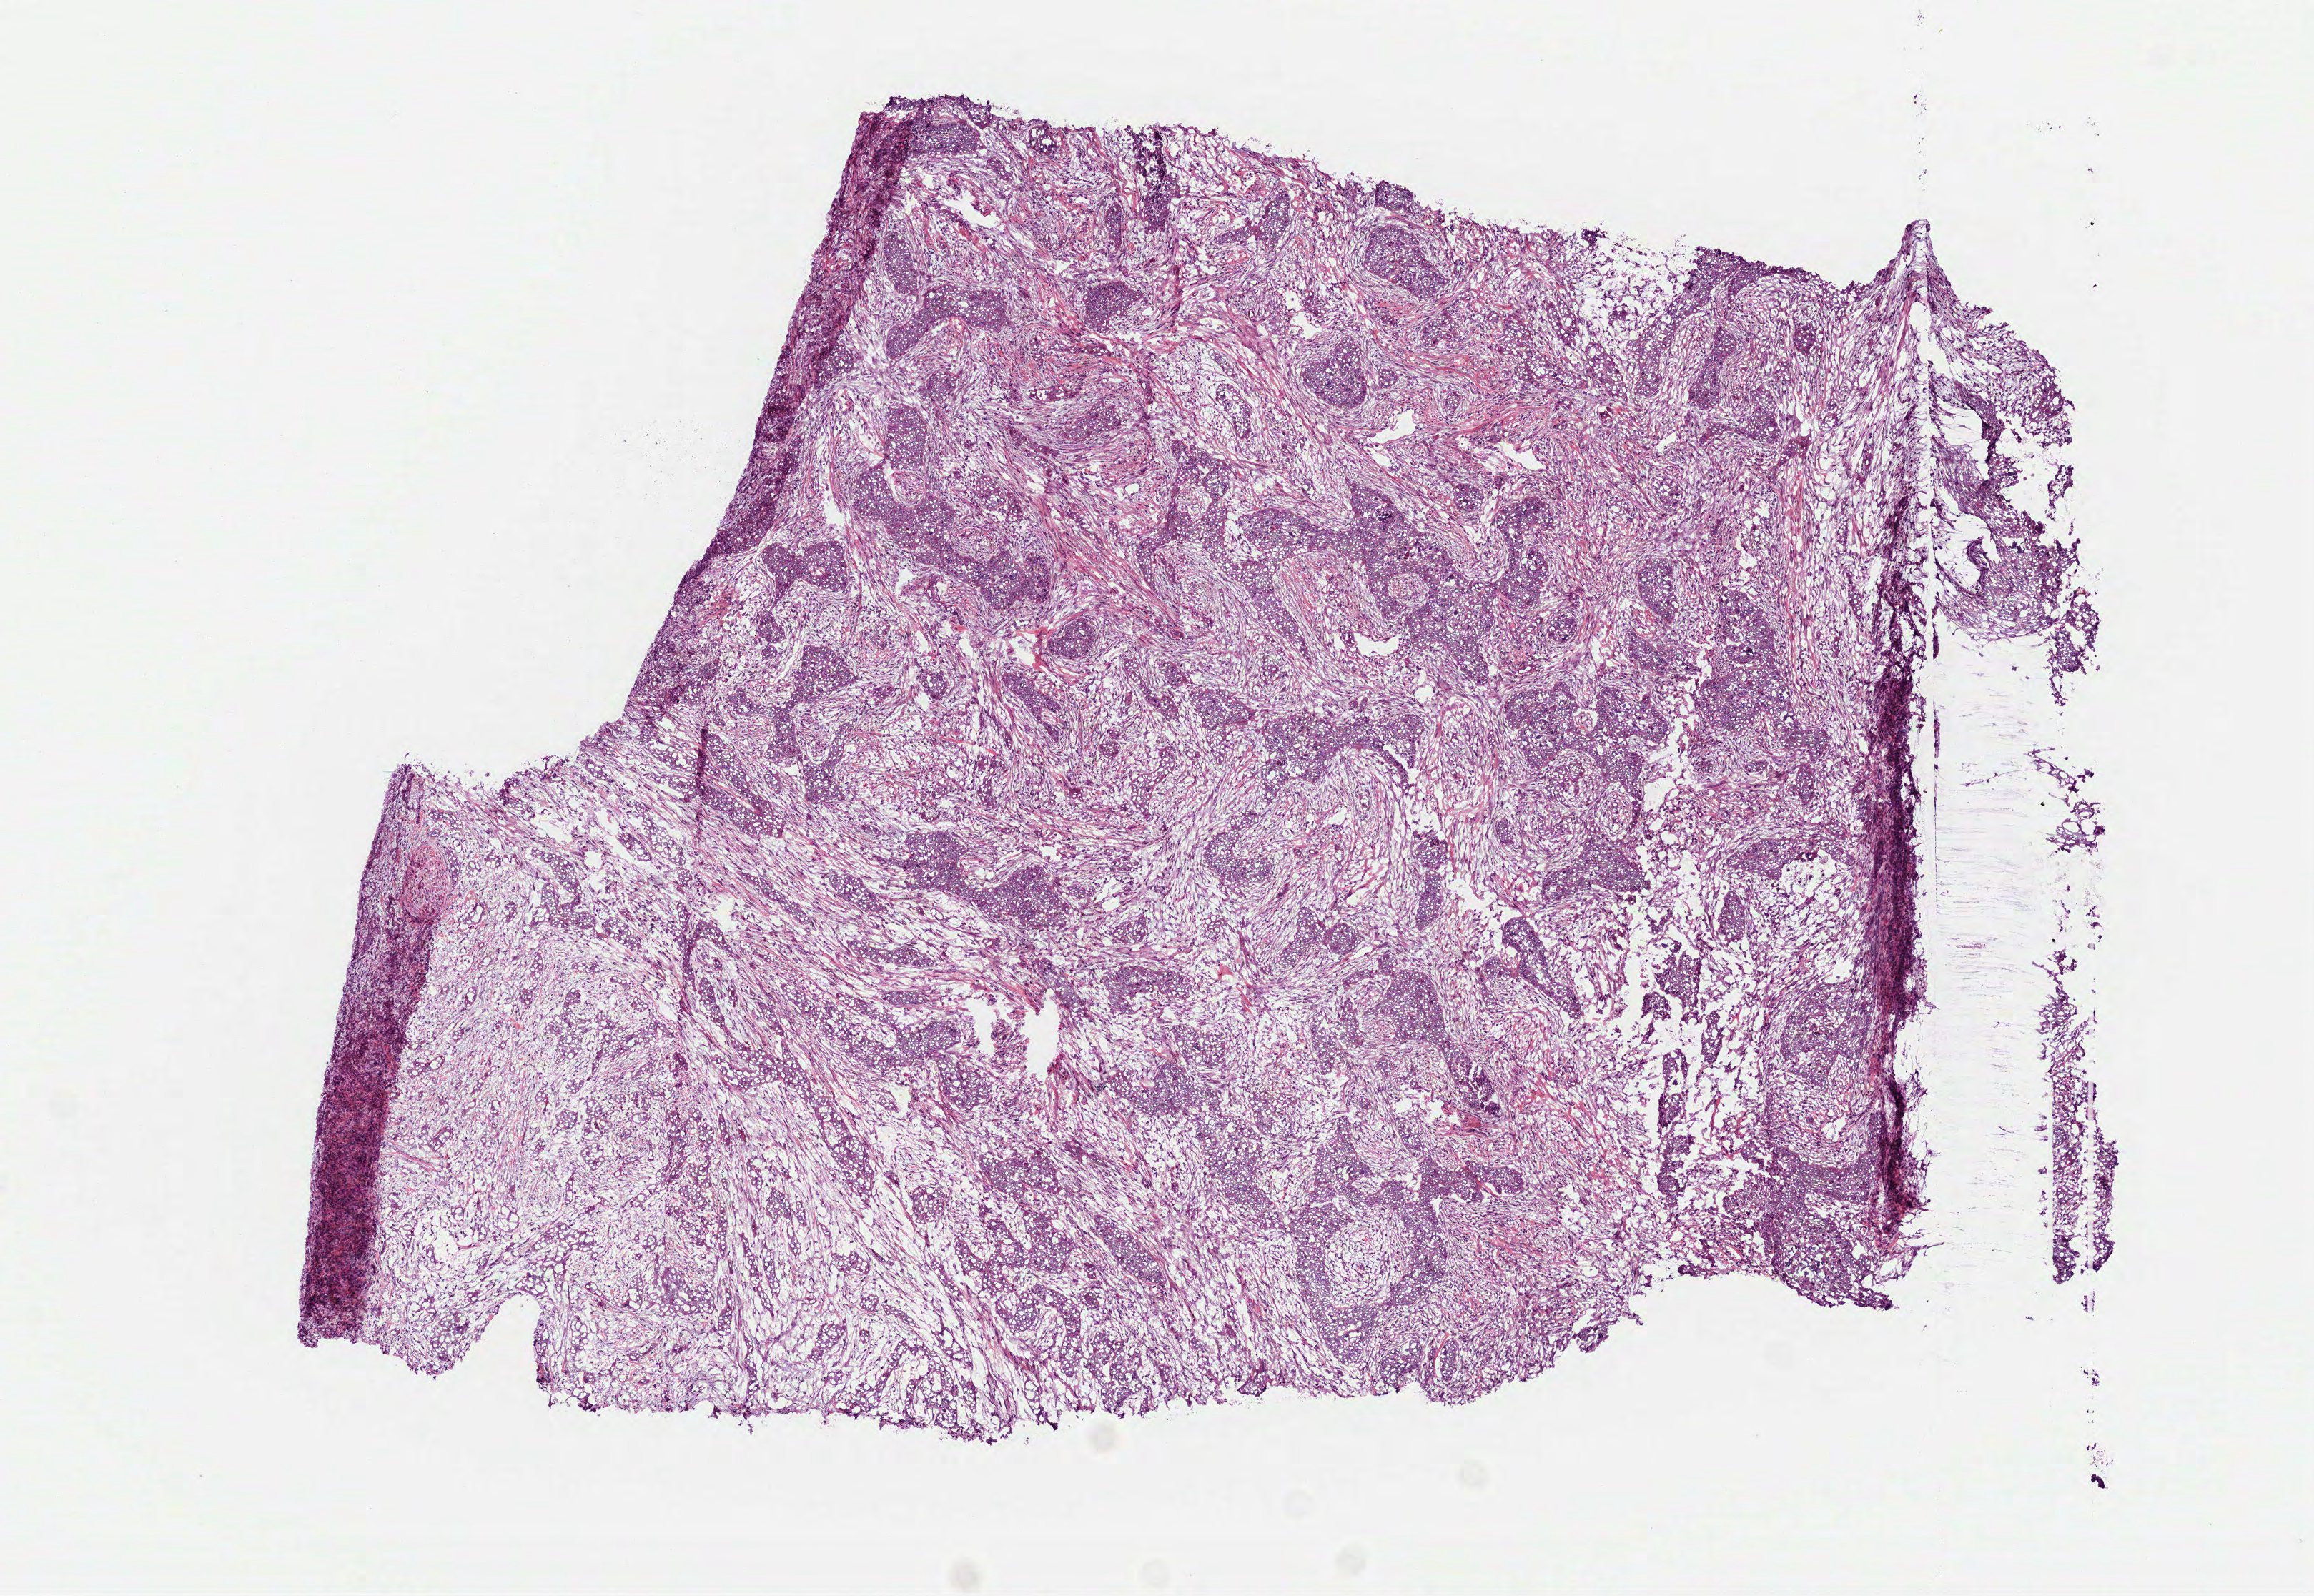
H&E whole-slide image, whole scanned area (about 6.5 x 4.5 mm, acquisition: 40x scan) shown as a low-resolution overview. Frozen section. Head and neck, primary tumour sample. Patient: male, age at initial diagnosis 51 years. Histologic grade: G3 (poorly differentiated). Composition of this section per pathologist review: tumour cells 100%, tumour nuclei 62%, normal cells 0%, stromal cells 0%, necrosis 0%. Infiltration values recorded for this section: lymphocyte infiltration 10%, monocyte infiltration 0%, neutrophil infiltration 5%.
Histologic diagnosis: Squamous cell carcinoma, NOS (tongue, NOS). AJCC pathologic stage: II (6th edition).